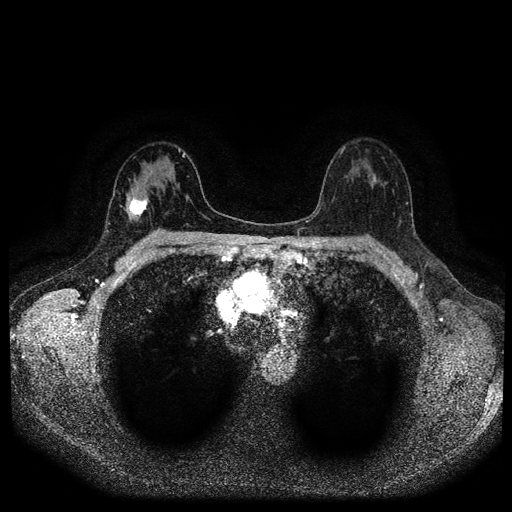
Breast MRI (dynamic contrast-enhanced, multi-phase), one axial slice. Position 63 of 116 along the scan axis. Dynamic contrast-enhanced series, time point 2 of 5 at this slice position (early post-contrast). 1.5 T. TE 2.7 ms, TR 5.4 ms. 2 mm slice thickness. 512 × 512 image matrix, field of view 330 × 330 mm. Female patient, age 42 years.
Structures marked on this image (semi-automatically segmented with operator editing):
- breast lesion (labelled 'tumour' in the annotation; benign lesions carry a separate 'benign' label): bounding box <127,195,150,219> (left, top, right, bottom; pixels)